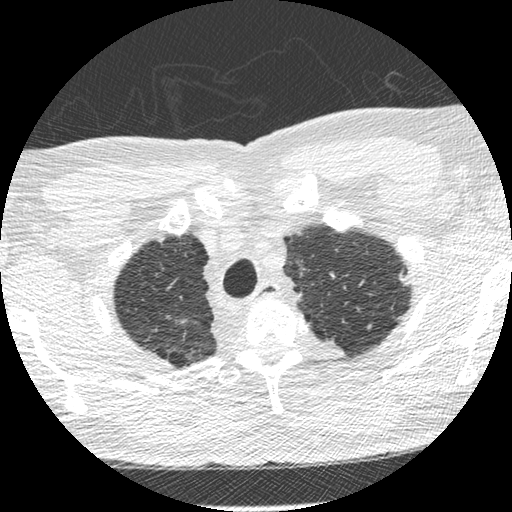
Low-dose screening chest CT, one axial slice. Position 244 of 275 along the scan axis. Reconstruction kernel STANDARD. Lung window (W 1500 / L -600 HU). 512 × 512 image matrix, field of view 330 × 330 mm.
Outlined on this slice (outlined manually by an expert reader):
- lesion 1 (tumor, upper lobe of left lung): bounding box [x1, y1, x2, y2] px = [399, 273, 410, 286]